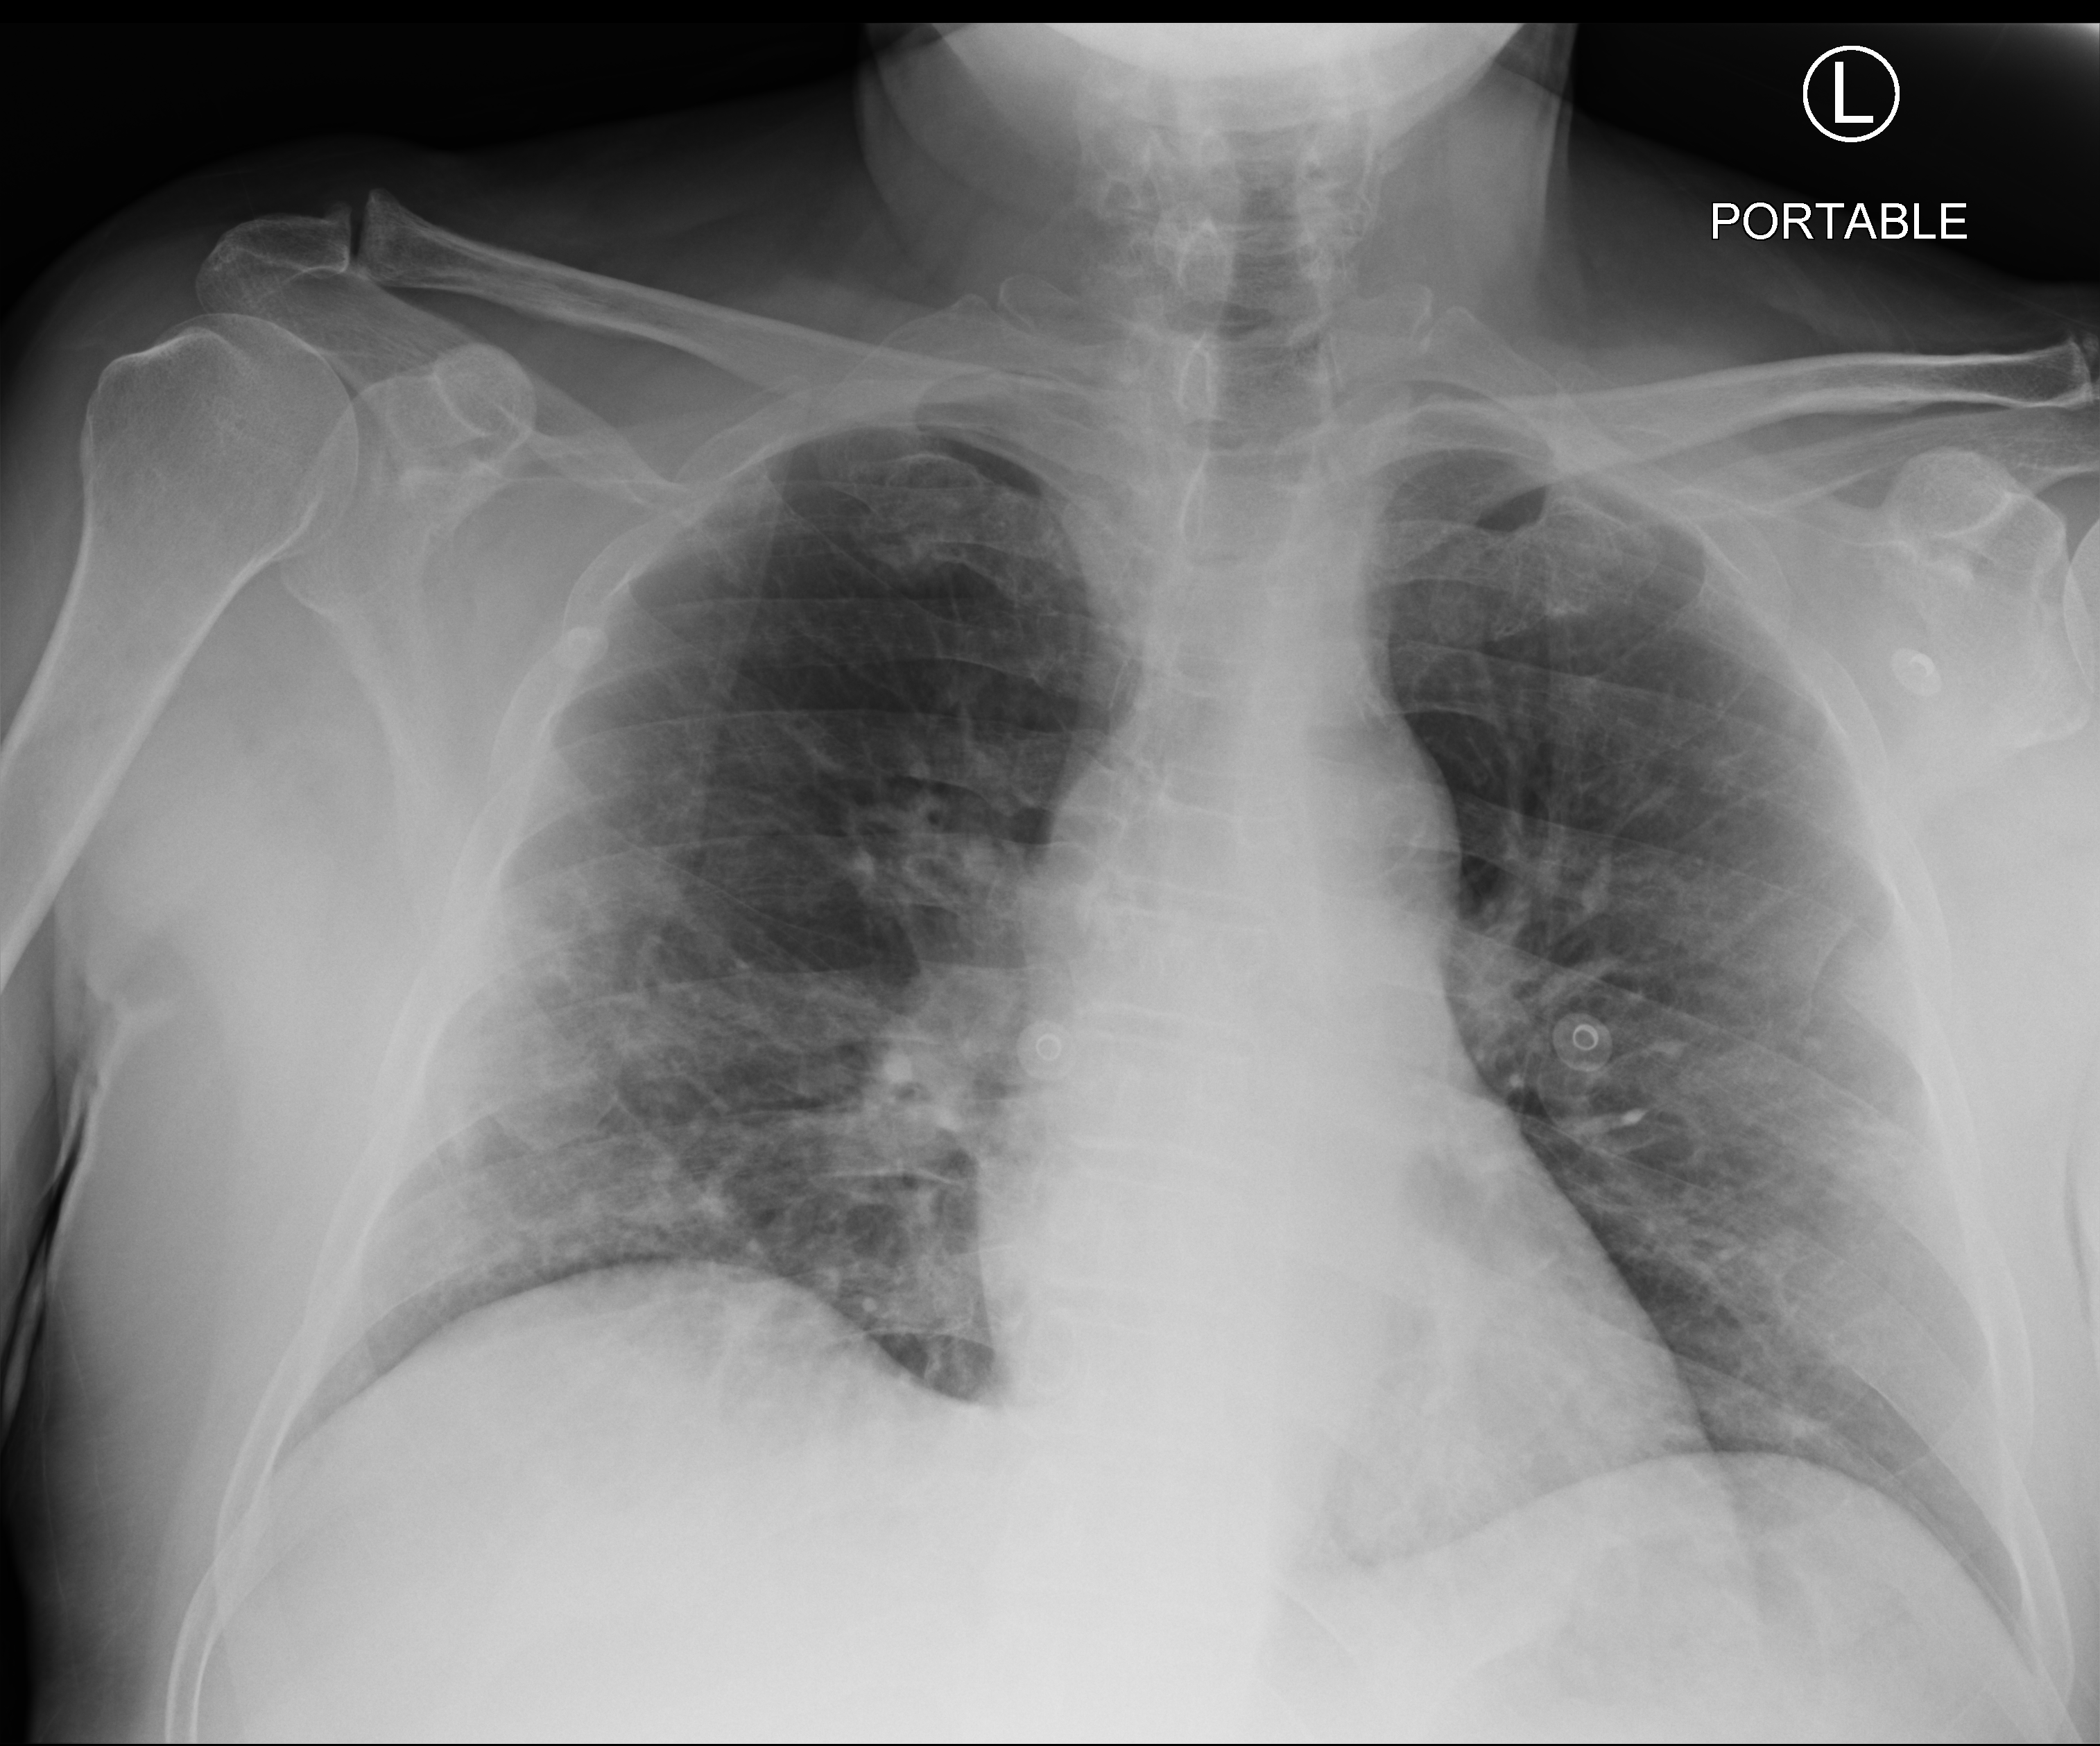
Chest X-ray (portable); anteroposterior (AP) projection. Patient hospitalised with COVID-19; male, aged 60–74 years.
From the hospital-stay record, not from the radiograph (when in the stay this image was taken is not recorded): admitted to intensive care during this hospital stay: no; chronic kidney disease (admission record): no.